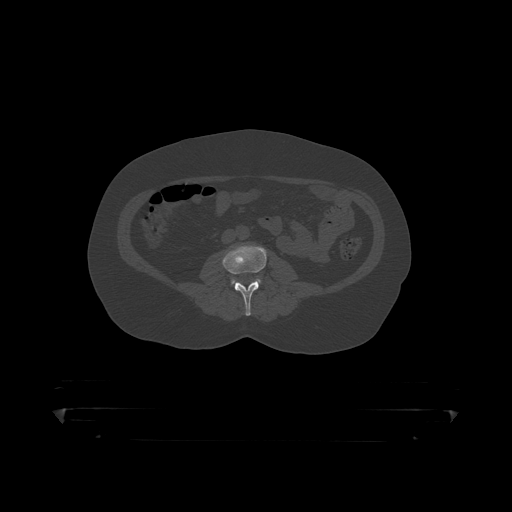
CT including the spine, one axial slice; slice 84 of 390 in the series (ordered by position); reconstruction kernel STANDARD; 120 kVp; bone window (W 1800 / L 400 HU); 1.25 mm slice thickness; 512 × 512 image matrix. Male patient, age 60 years. From the clinical record (not read from this slice): primary cancer: prostate.
Outlined on this slice (semi-automatically segmented with operator editing):
- L3 vertebra: box from (x=223, y=245) to (x=267, y=316) px